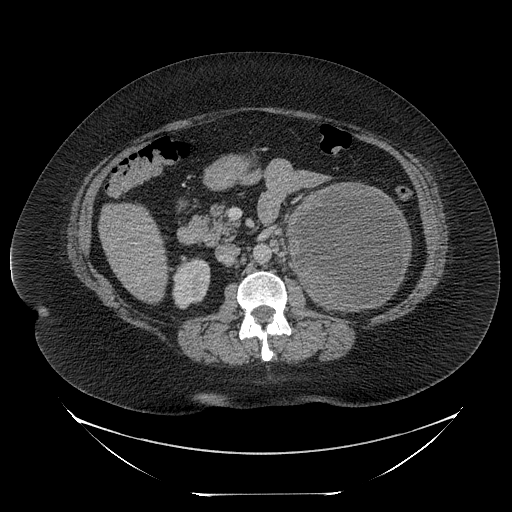
Contrast-enhanced abdominal CT, one axial slice. Slice 127 of 205 in the series (ordered by position). Intravenous contrast given. Soft-tissue window (W 400 / L 40 HU). 2.5 mm slice thickness. 512 × 512 image matrix, field of view 500 × 500 mm. Patient: female, 53 years. From the clinical record (not read from this slice): diagnosis: adrenocortical carcinoma; tumour side: left adrenal; tumour size at pathology: 17 cm; Ki-67 index: 20 %; stage (as recorded): 3.
Structures marked on this image (semi-automatically segmented with operator editing):
- mass: box from (x=292, y=185) to (x=409, y=309) px